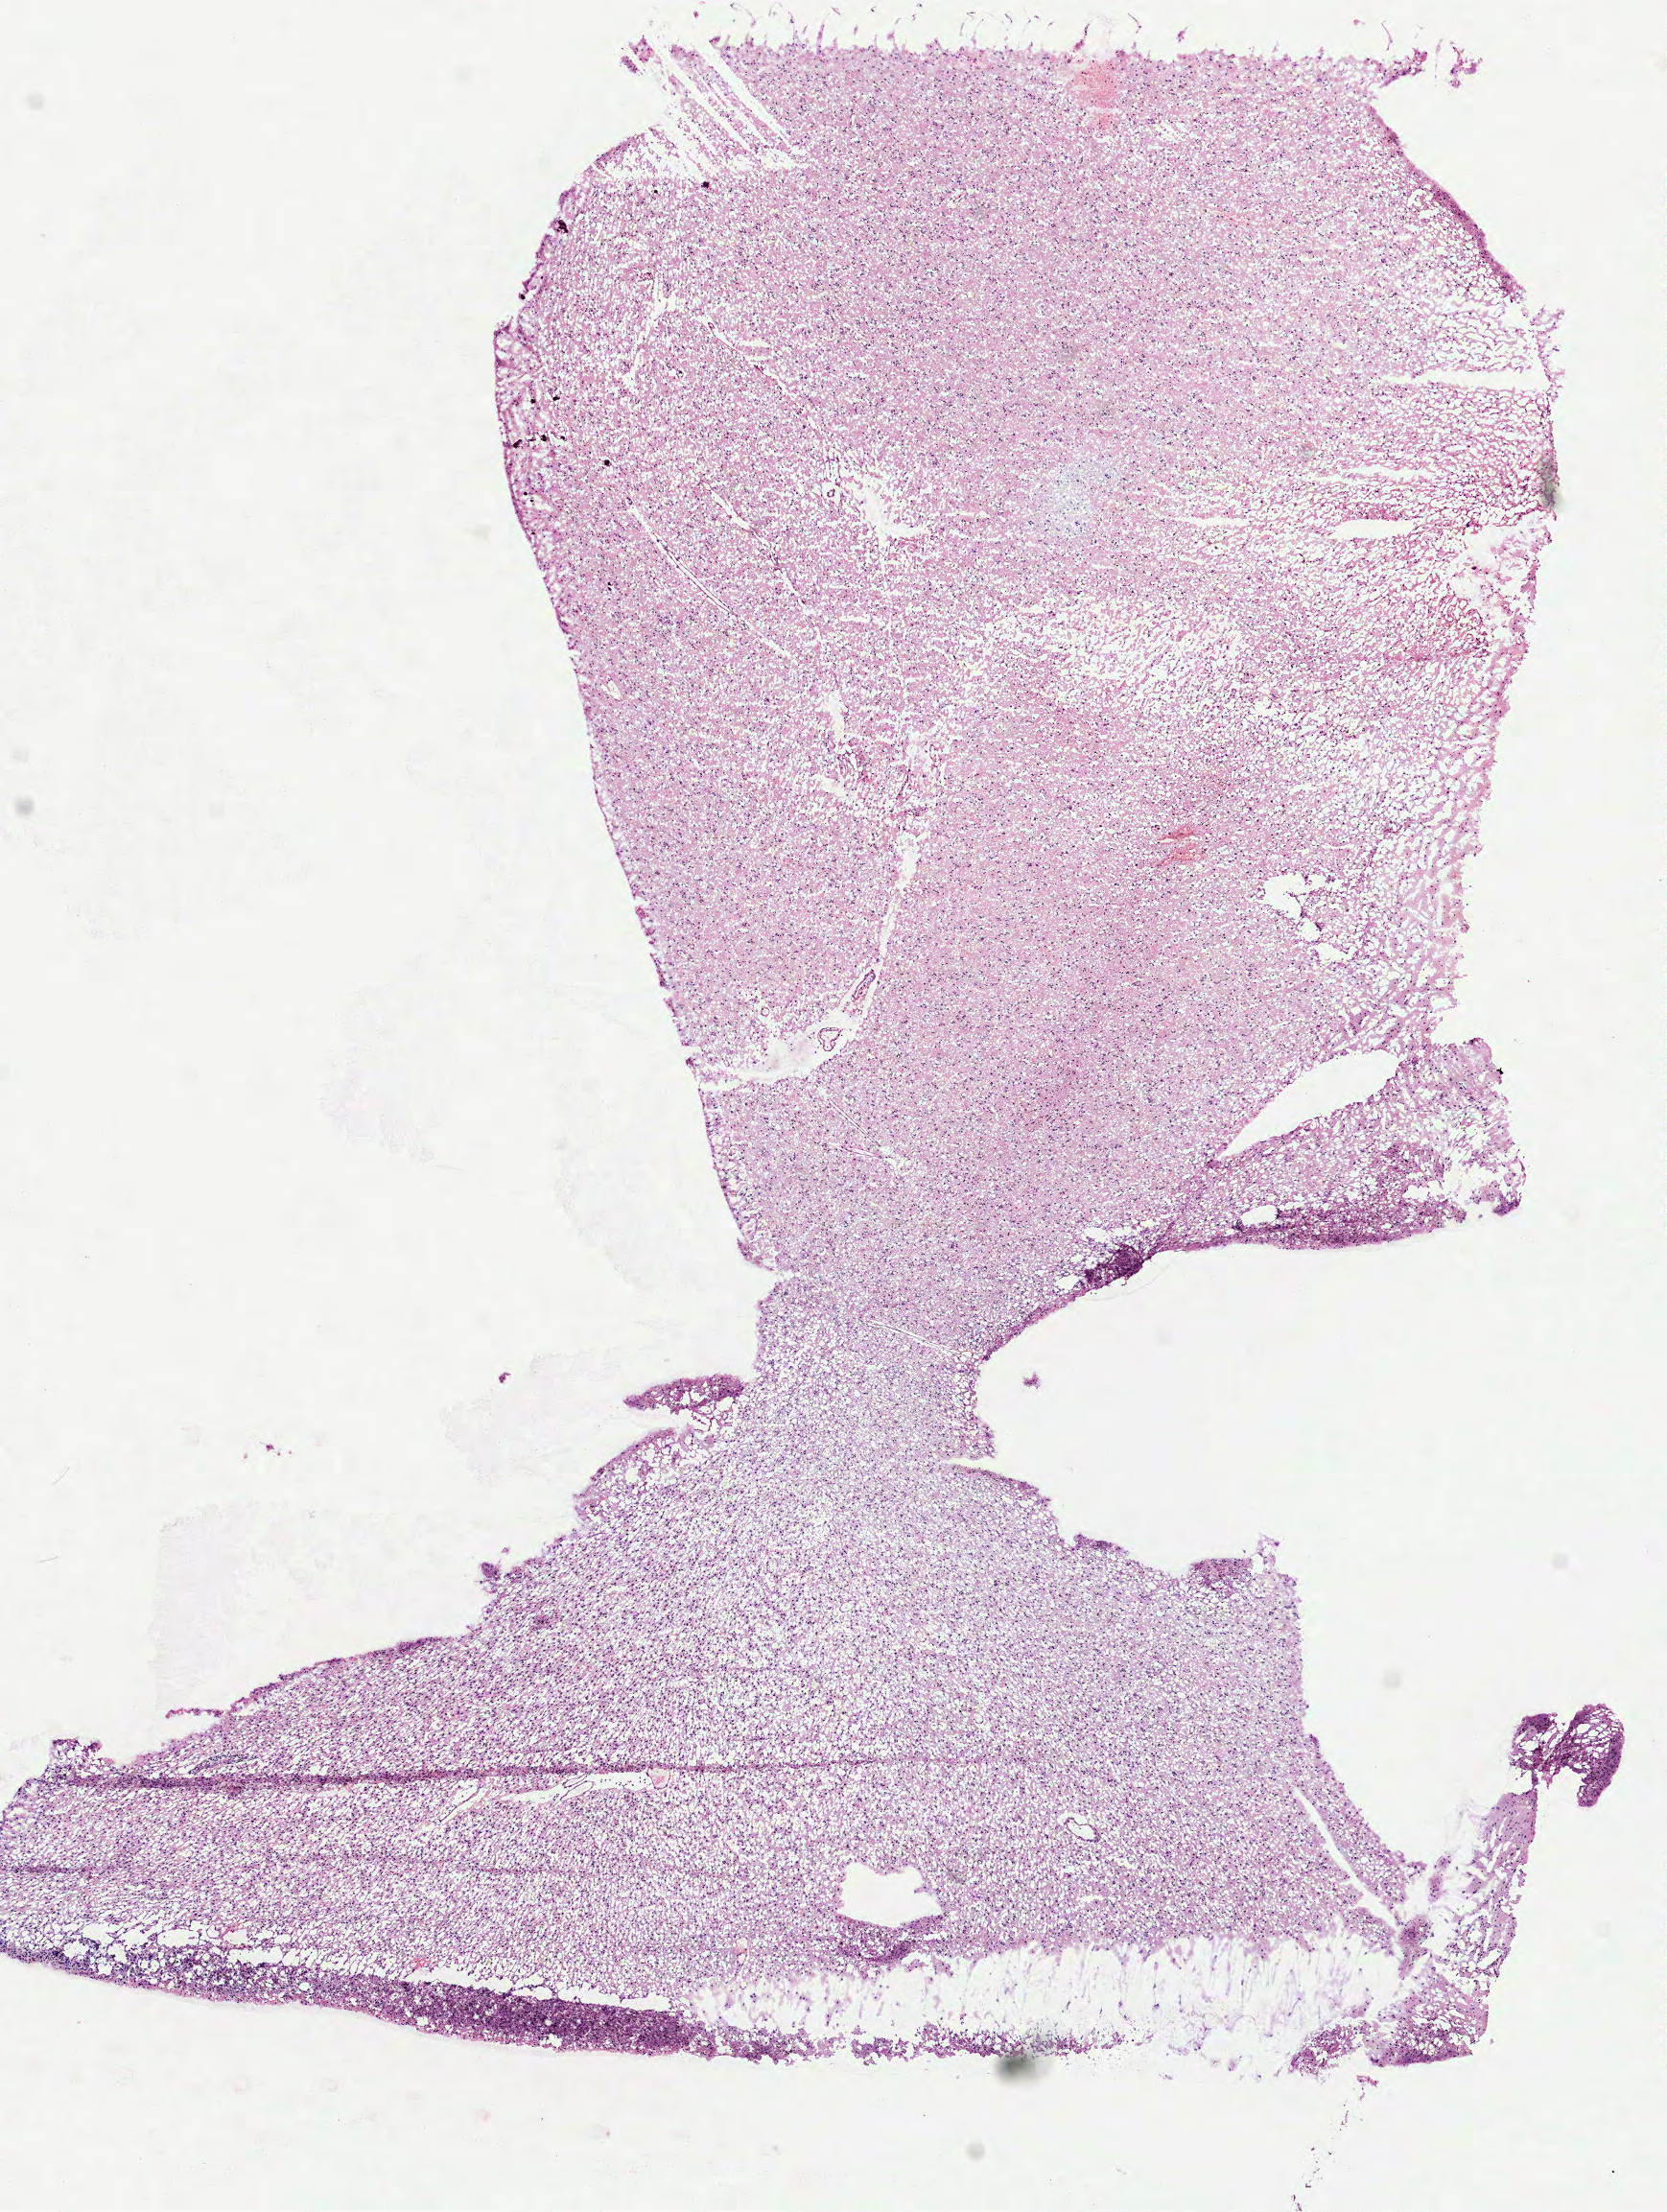
Hematoxylin and eosin (H&E) stained whole-slide image — whole scanned area (about 7.0 x 9.3 mm) shown as a low-resolution overview. Frozen section. Brain, primary tumour sample. Male patient; age at initial diagnosis 33 years. Histologic grade: G2 (moderately differentiated). Composition of this section per pathologist review: tumour cells 100%, tumour nuclei 65%, normal cells 0%, stromal cells 0%, necrosis 0%.
Pathologic diagnosis: Oligodendroglioma, NOS. Laterality: right.